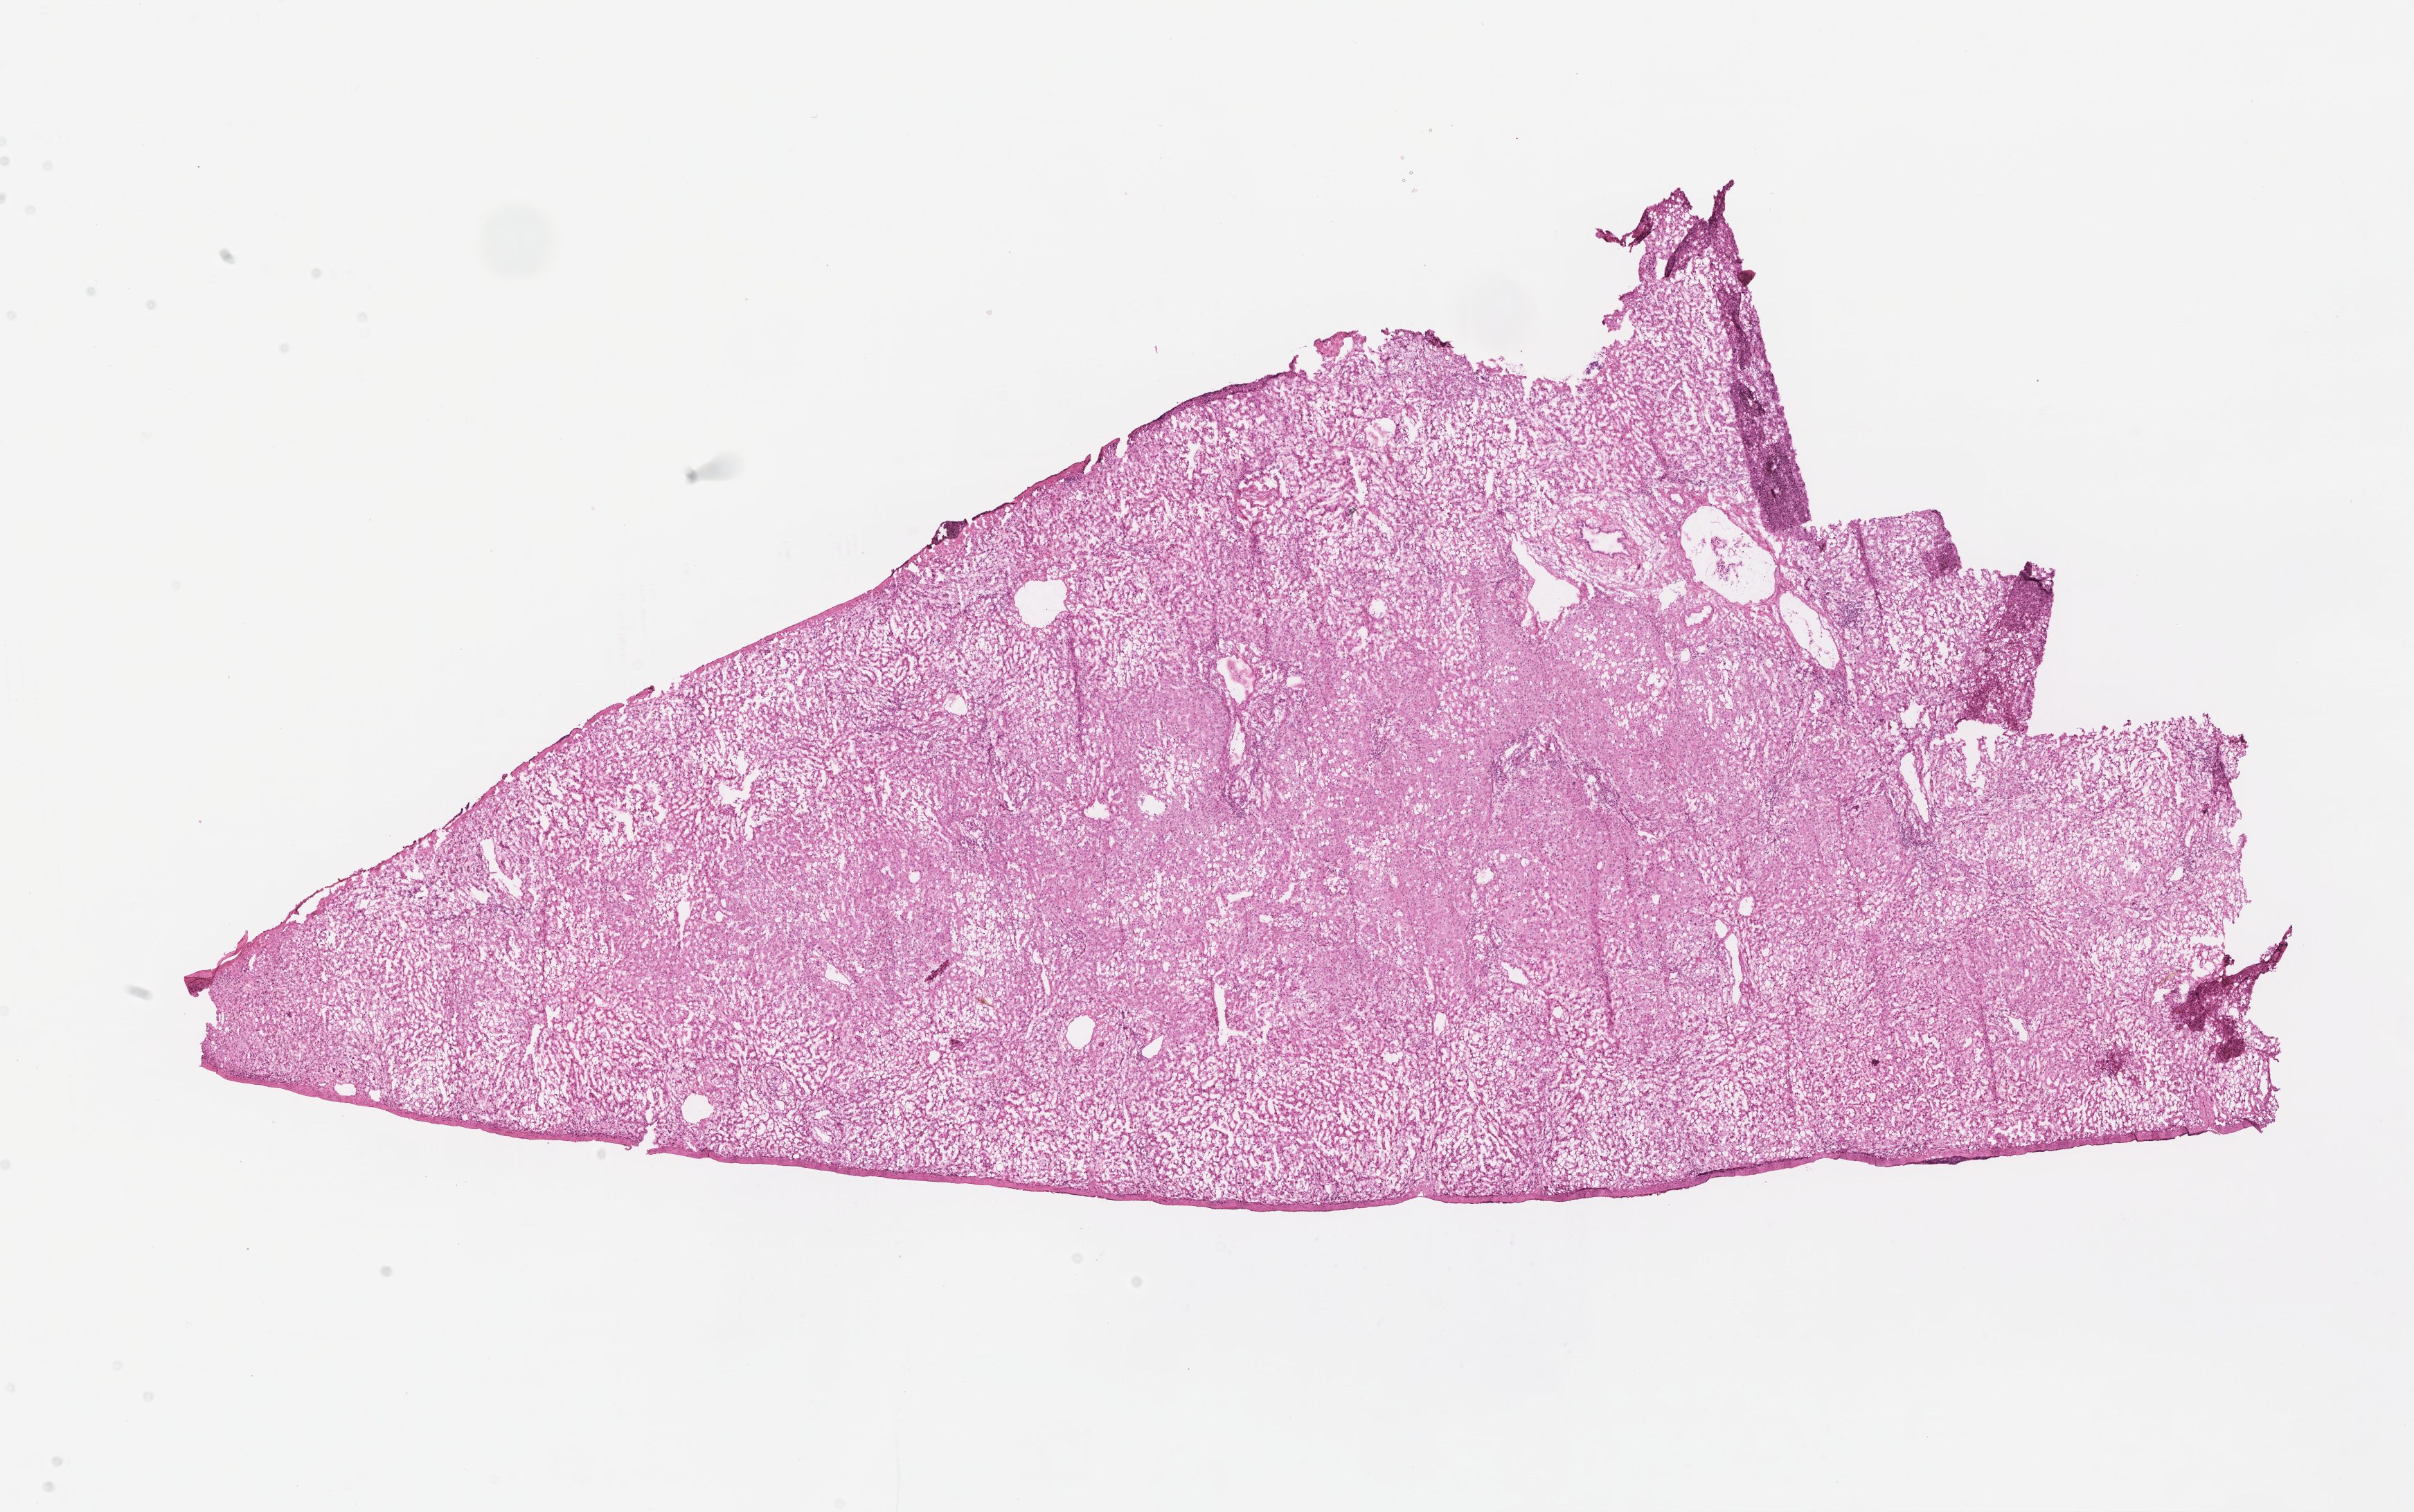
Hematoxylin and eosin (H&E) whole-slide image, shown as a low-resolution overview of the whole scanned area (about 14.1 x 8.8 mm); frozen section; non-tumor (normal tissue) sample from a patient with adenocarcinoma, NOS; anatomic site: colon. Male patient; age at initial diagnosis 70 years. Slide review estimates, as recorded: tumor cells 0%, tumor nuclei 0%, stromal cells 0%, necrosis 0%, normal cells 100%. Inflammatory infiltration, as recorded: lymphocyte infiltration 5%, monocyte infiltration 5%, neutrophil infiltration 2%.
This section: non-tumor tissue sample; the patient's diagnosis is given above. Section: top of the tissue portion.